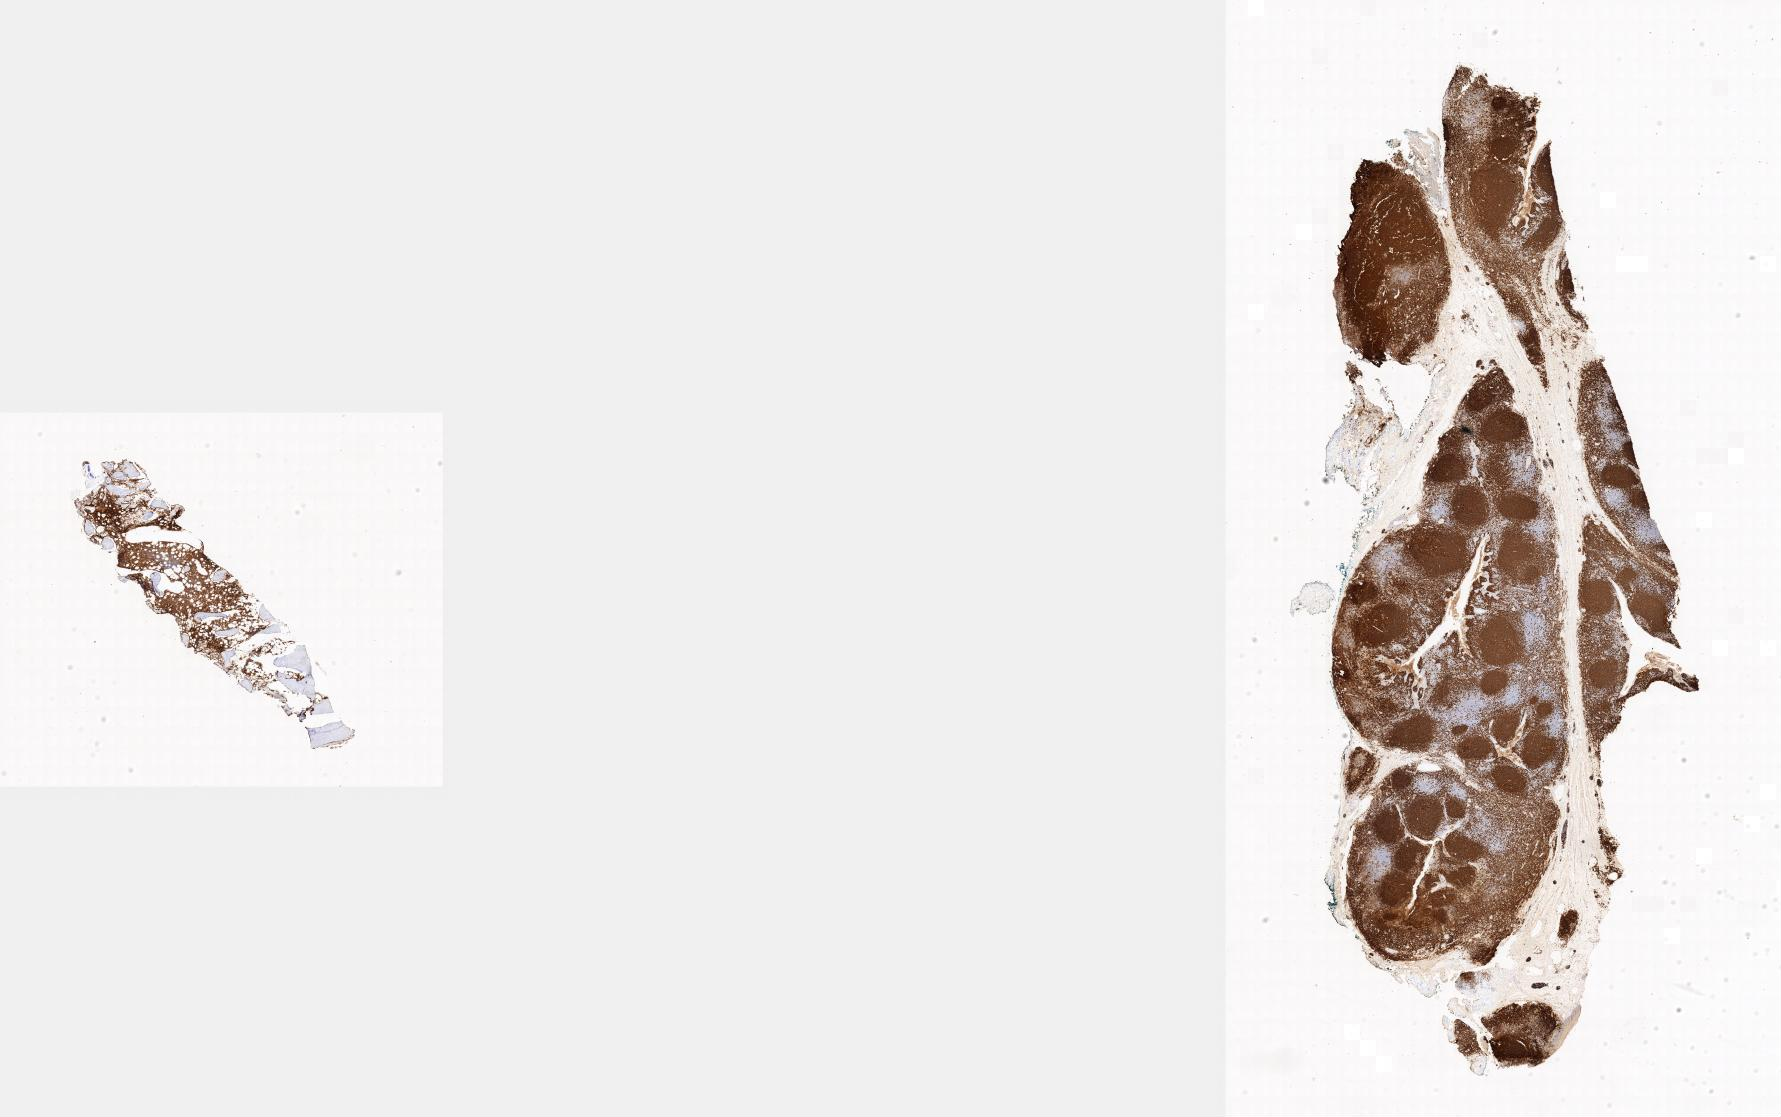
IHC for CD20, whole-slide image — shown as a low-resolution overview of the whole scanned area, tumor tissue, site: bone marrow. Patient: female, age at initial diagnosis 4 years.
Histologic diagnosis: Burkitt lymphoma, NOS.